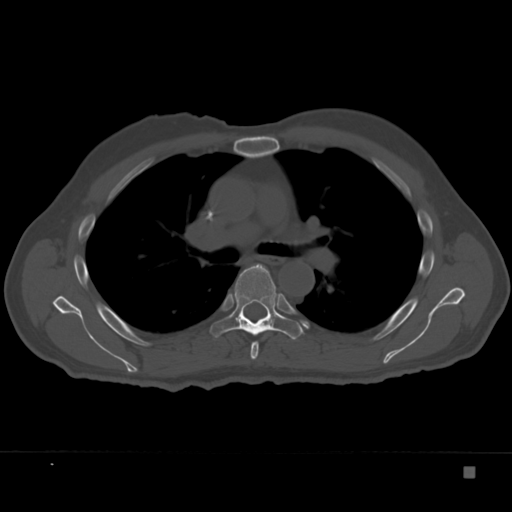
CT including the spine, one axial slice; slice 244 of 332 in the series (ordered by position); 120 kVp; bone window (W 1800 / L 400 HU); 512 × 512 image matrix, field of view 389 × 389 mm. Male patient, age 72 years. Case-level facts recorded for this patient, not image findings: primary cancer: skeletal.
Outlined on this slice (semi-automatically segmented with operator editing):
- T5 vertebra: bounding box <250,341,259,360> (left, top, right, bottom; pixels)
- T6 vertebra: <209,264,304,340>